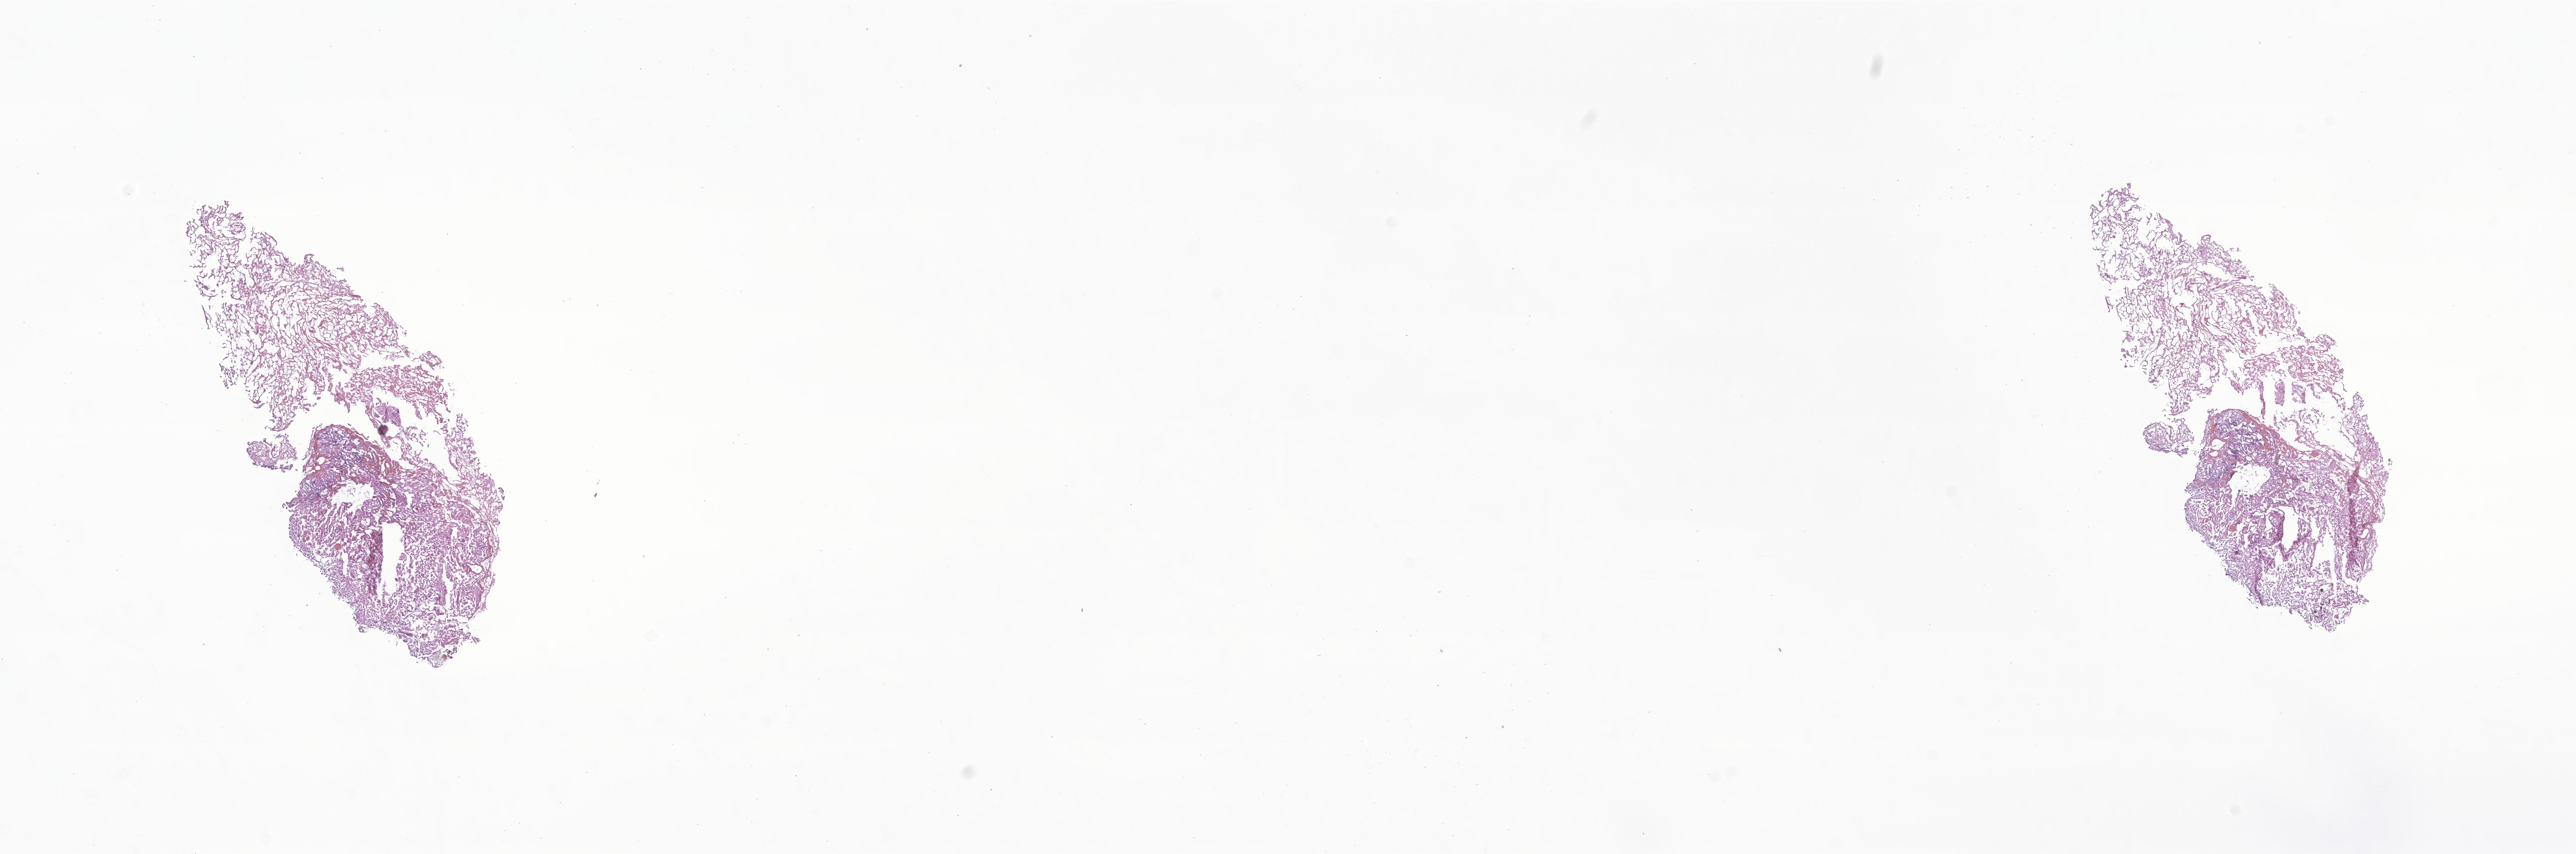
Digitized H&E-stained section of tumor tissue from the cerebellum — whole scanned area (about 25.8 x 8.6 mm) shown as a low-resolution overview; cryosection (OCT / tissue freezing medium). Patient male; age 61 months.
Diagnosis: Atypical meningioma.